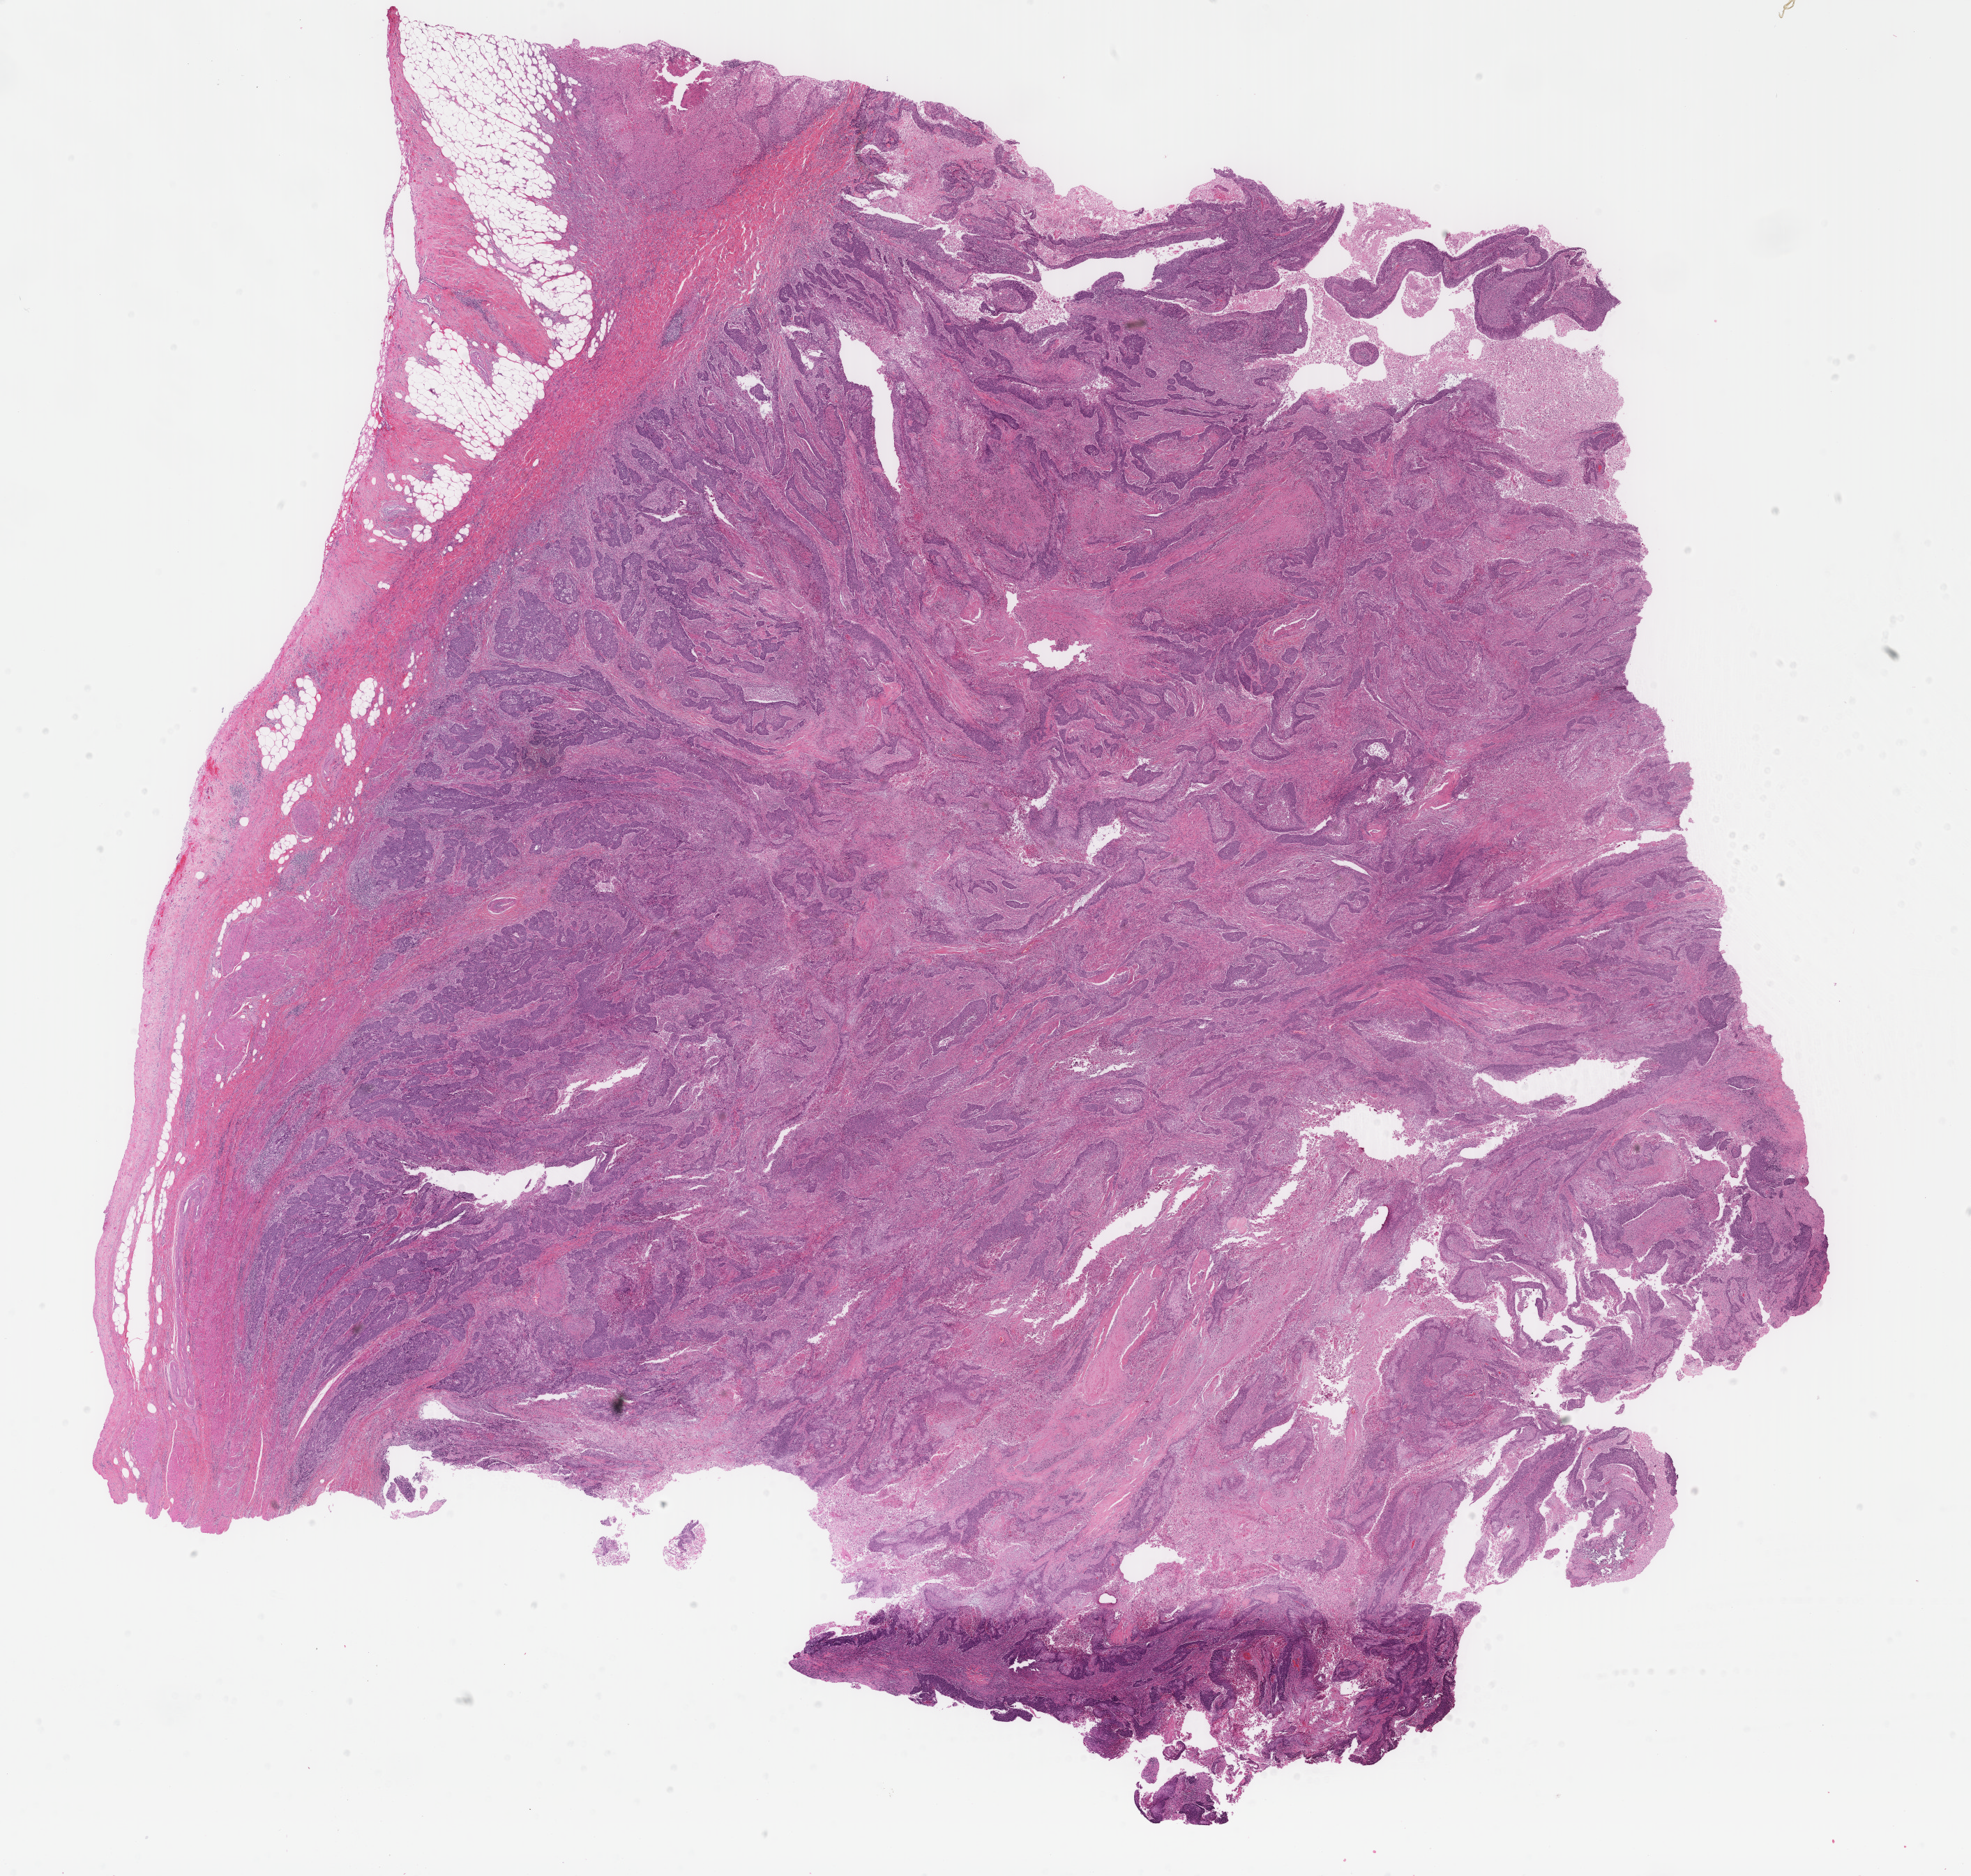
Whole-slide histology image, H&E — a low-resolution overview of the entire scanned area, about 22.4 x 21.3 mm (slide scanned at 40x). Formalin-fixed paraffin-embedded (FFPE) diagnostic section. Bladder, primary tumour sample. Male, age 85 years at initial diagnosis.
Diagnosis: Transitional cell carcinoma.